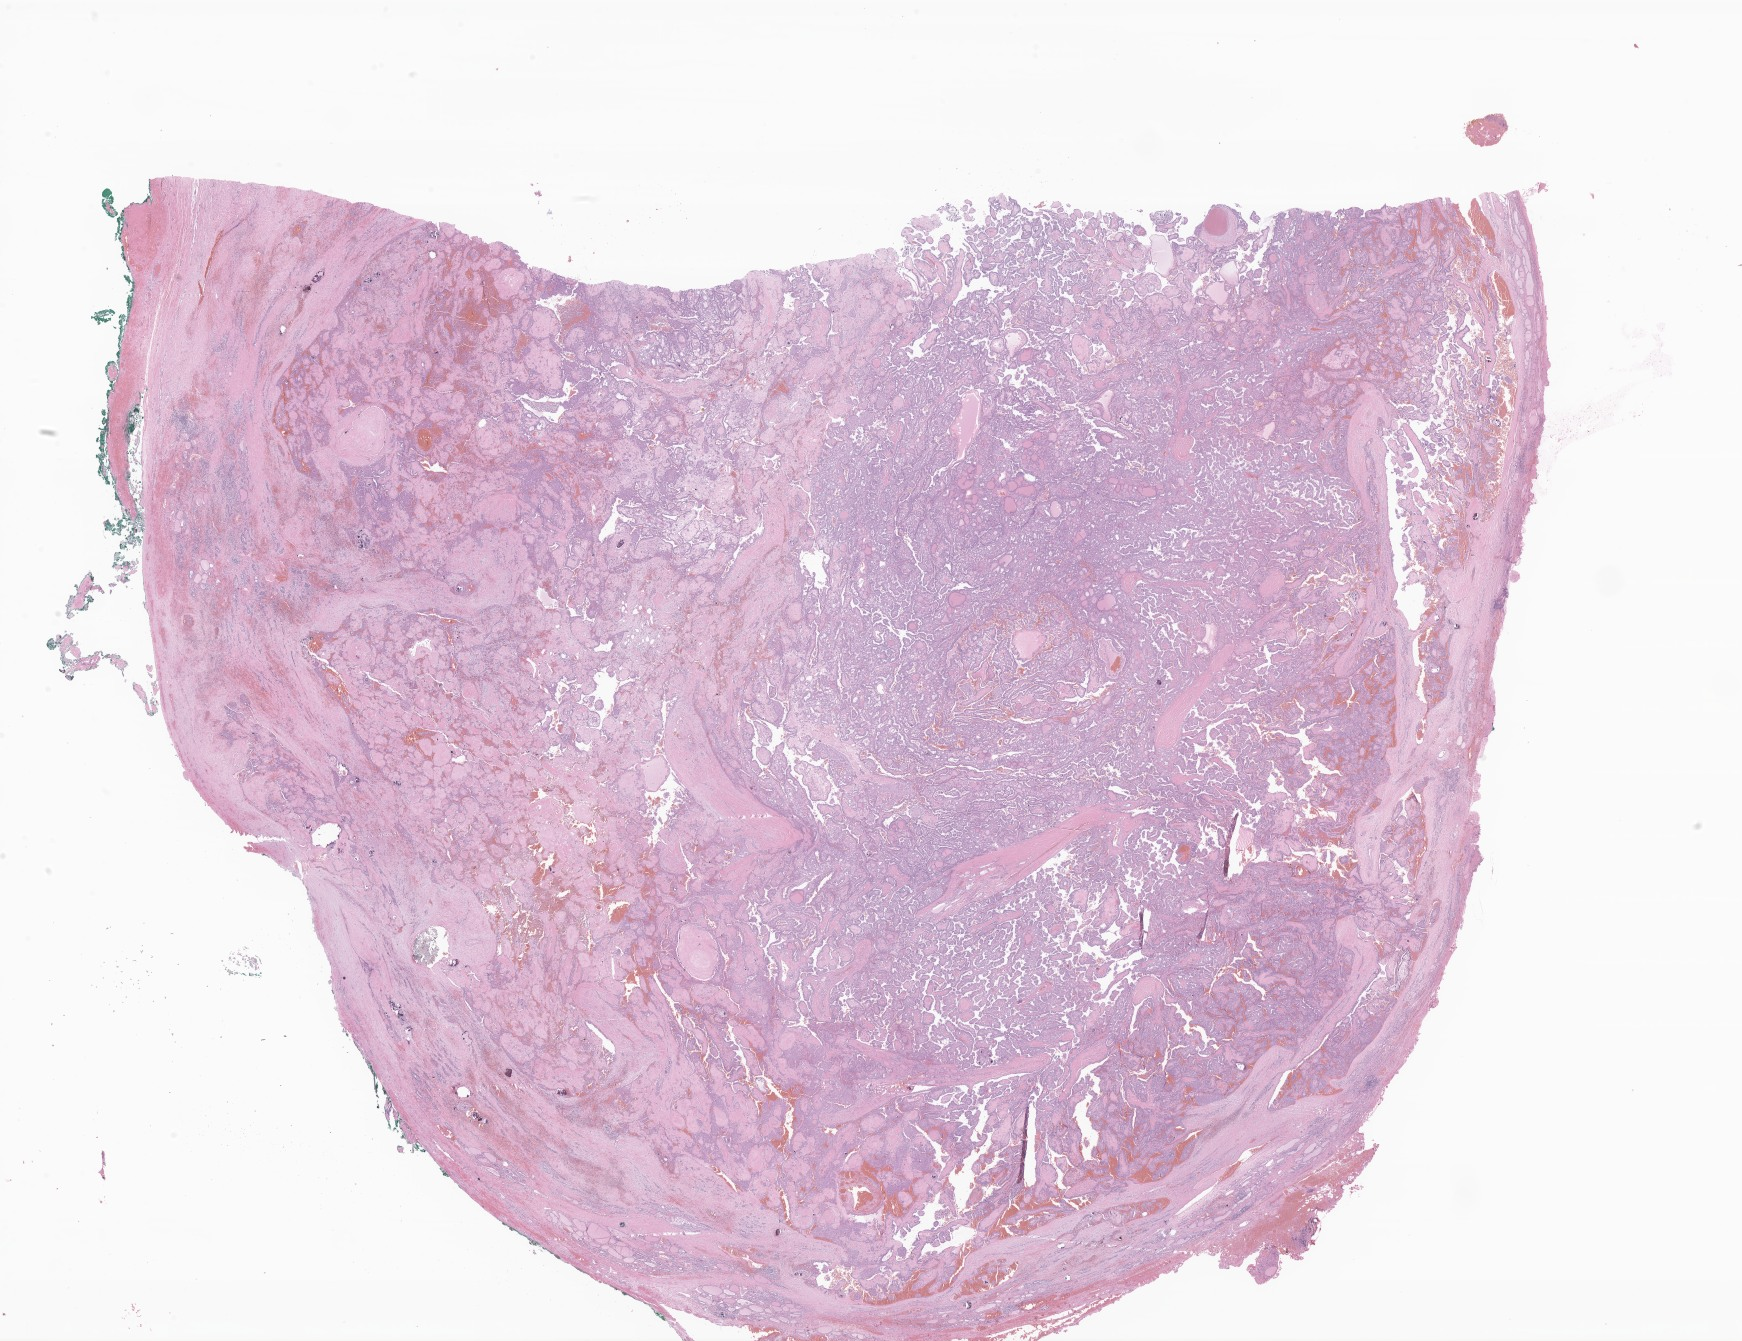
Whole-slide image, haematoxylin and eosin stain of tumor tissue from the thyroid — whole scanned area (about 29.4 x 22.6 mm) shown as a low-resolution overview, formalin-fixed, paraffin-embedded (FFPE) tissue. Patient male; age 192 months (16 years).
Recorded diagnosis: Papillary adenocarcinoma, NOS.